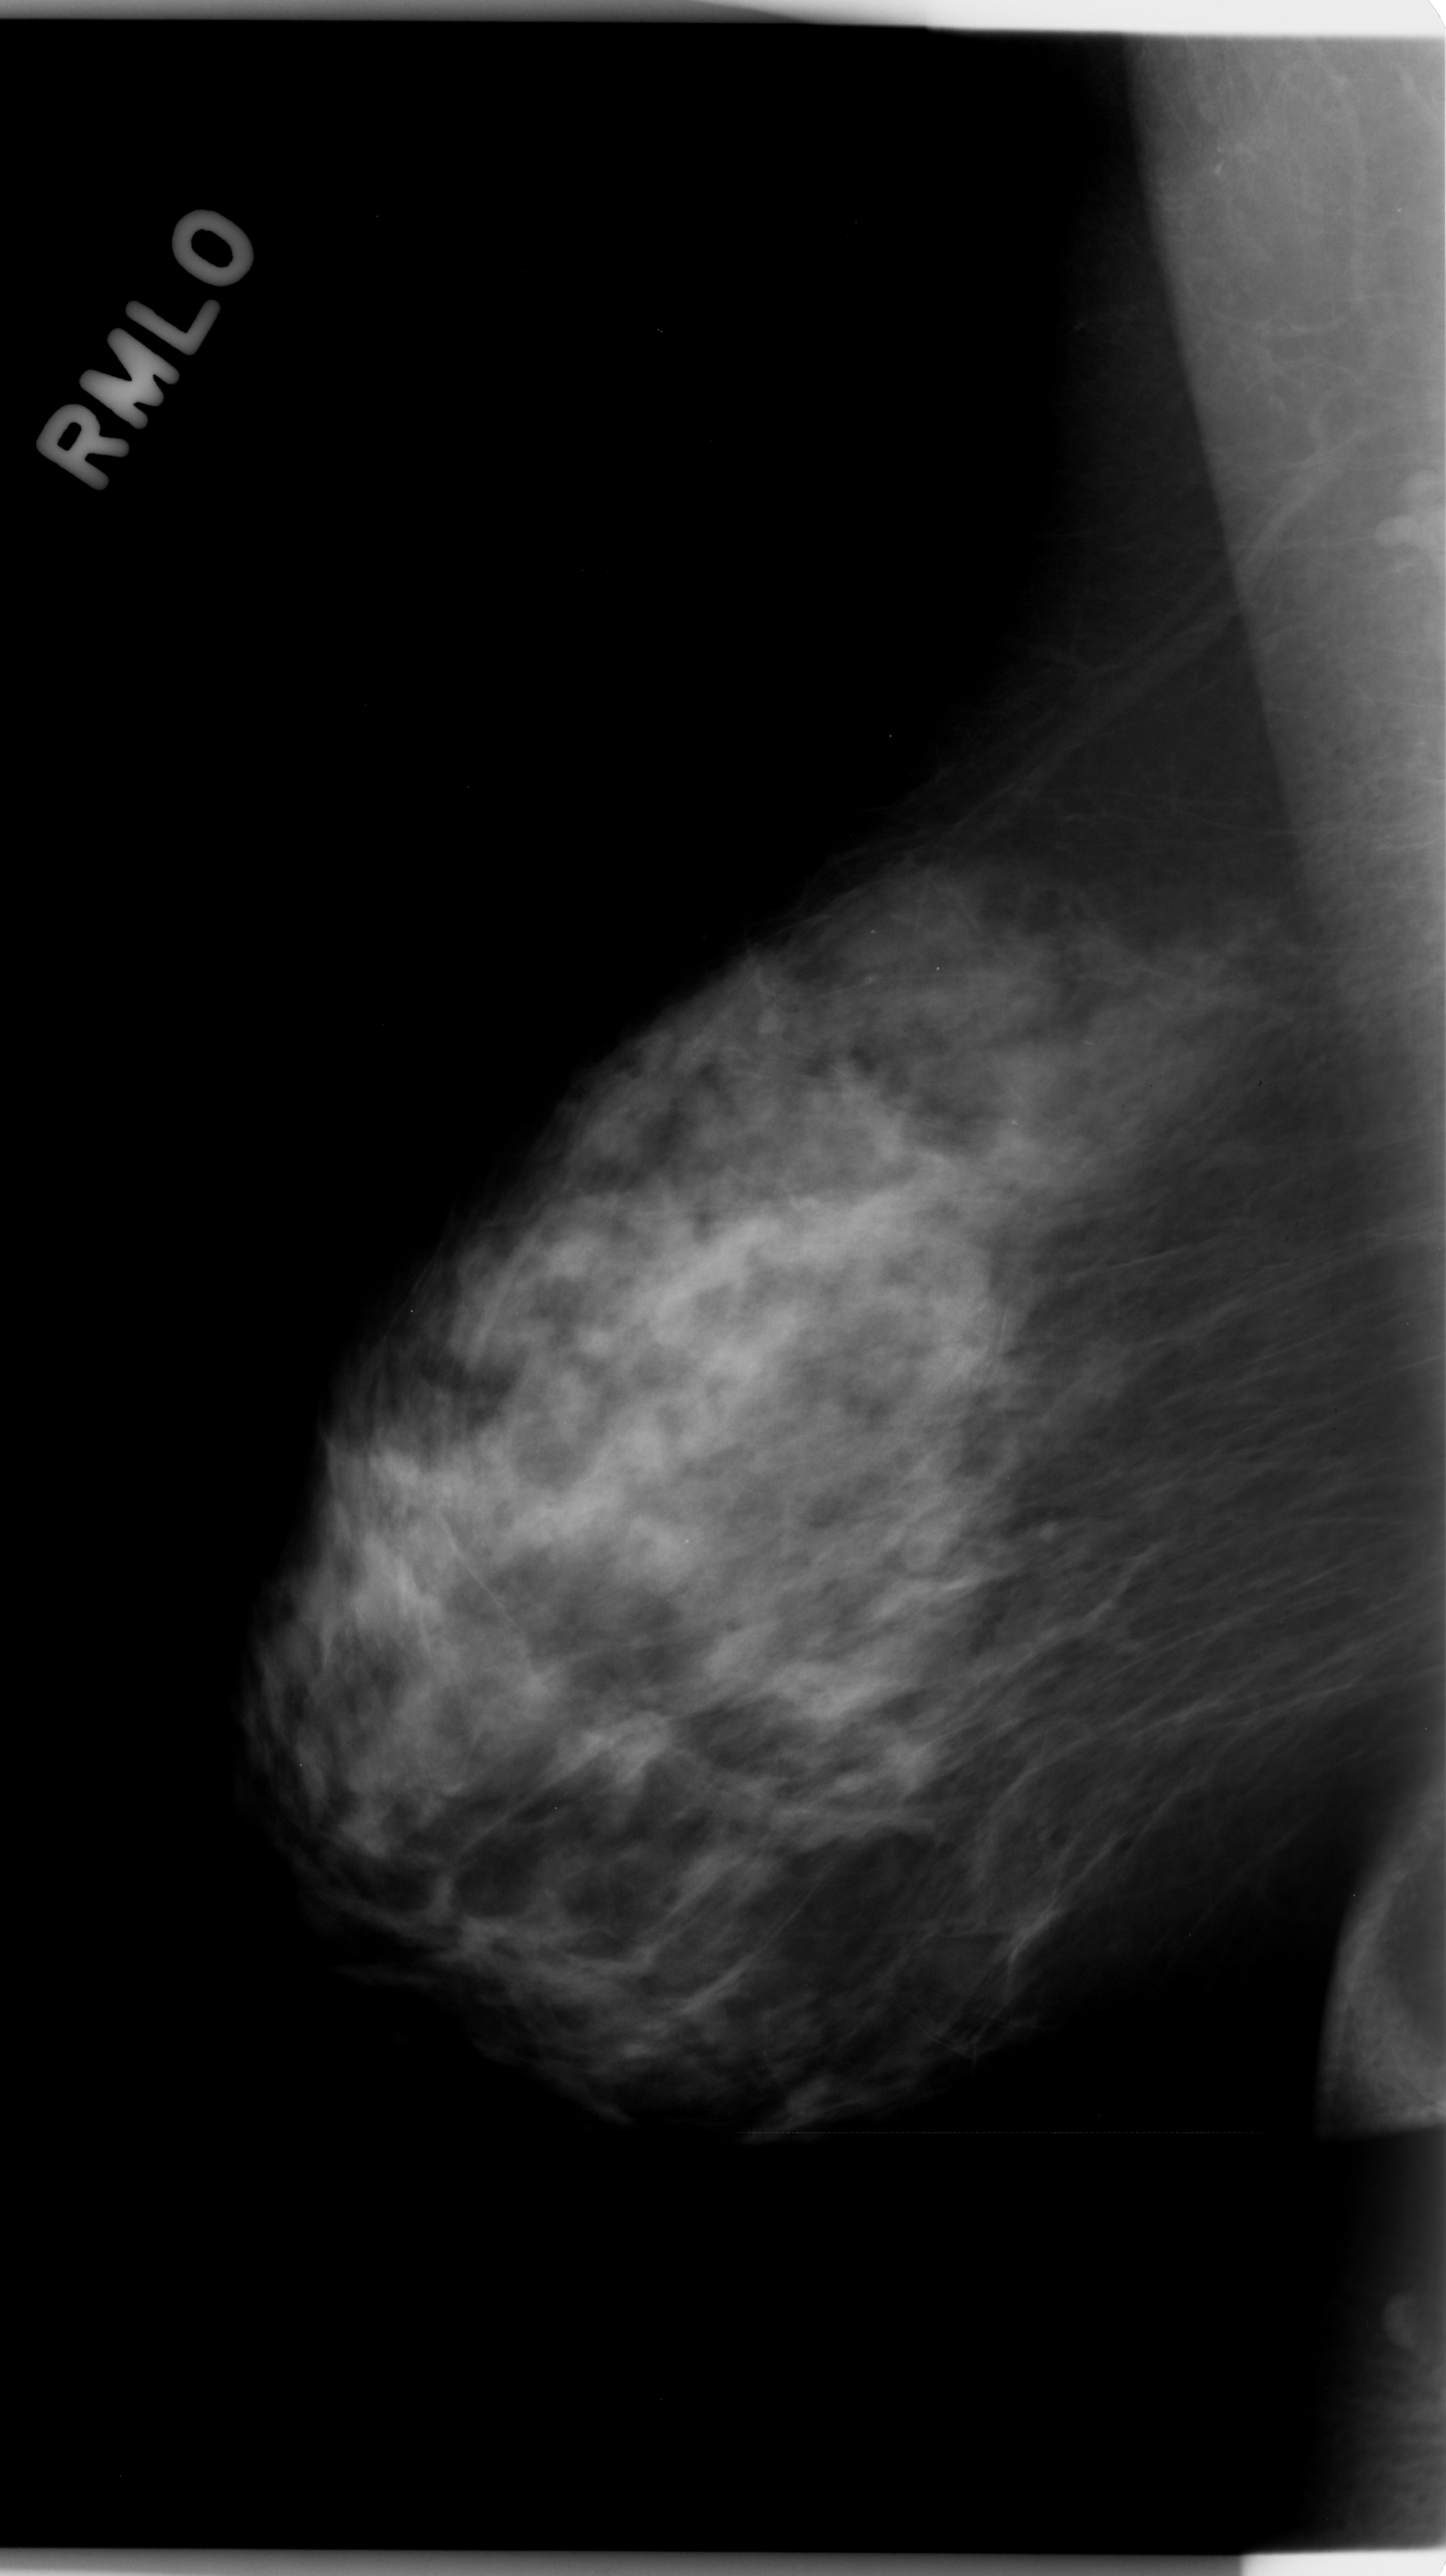
Digitized screen-film mammogram, right breast, MLO view.
Abnormality record for this image: calcifications, morphology amorphous, distribution clustered; BI-RADS assessment category 4; subtlety rating 2 on a 1 (subtle) to 5 (obvious) scale; pathology (as recorded): benign.